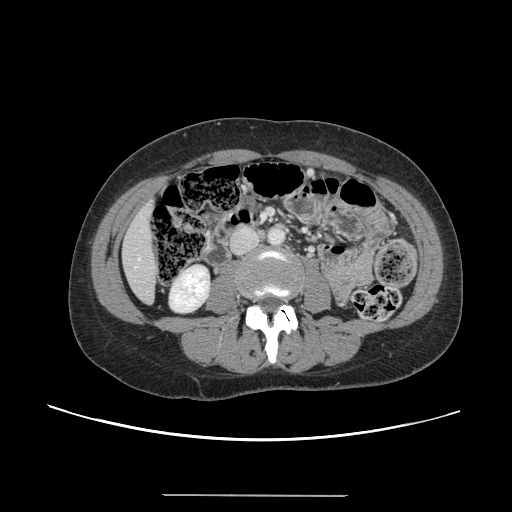
Contrast-enhanced abdominal CT, one axial slice; position 29 of 144 along the scan axis; intravenous contrast given; soft-tissue window (W 400 / L 40 HU); 2.5 mm slice thickness; 512 × 512 image matrix, field of view 380 × 380 mm. Female patient, age 53 years. From the clinical record (not read from this slice): diagnosis: colorectal cancer liver metastases, imaged before liver resection.
Outlined on this slice (expert manual segmentation):
- liver: bounding box <124,205,158,301> (left, top, right, bottom; pixels)
- planned liver remnant (the part of the liver to remain after resection): <123,205,157,302>